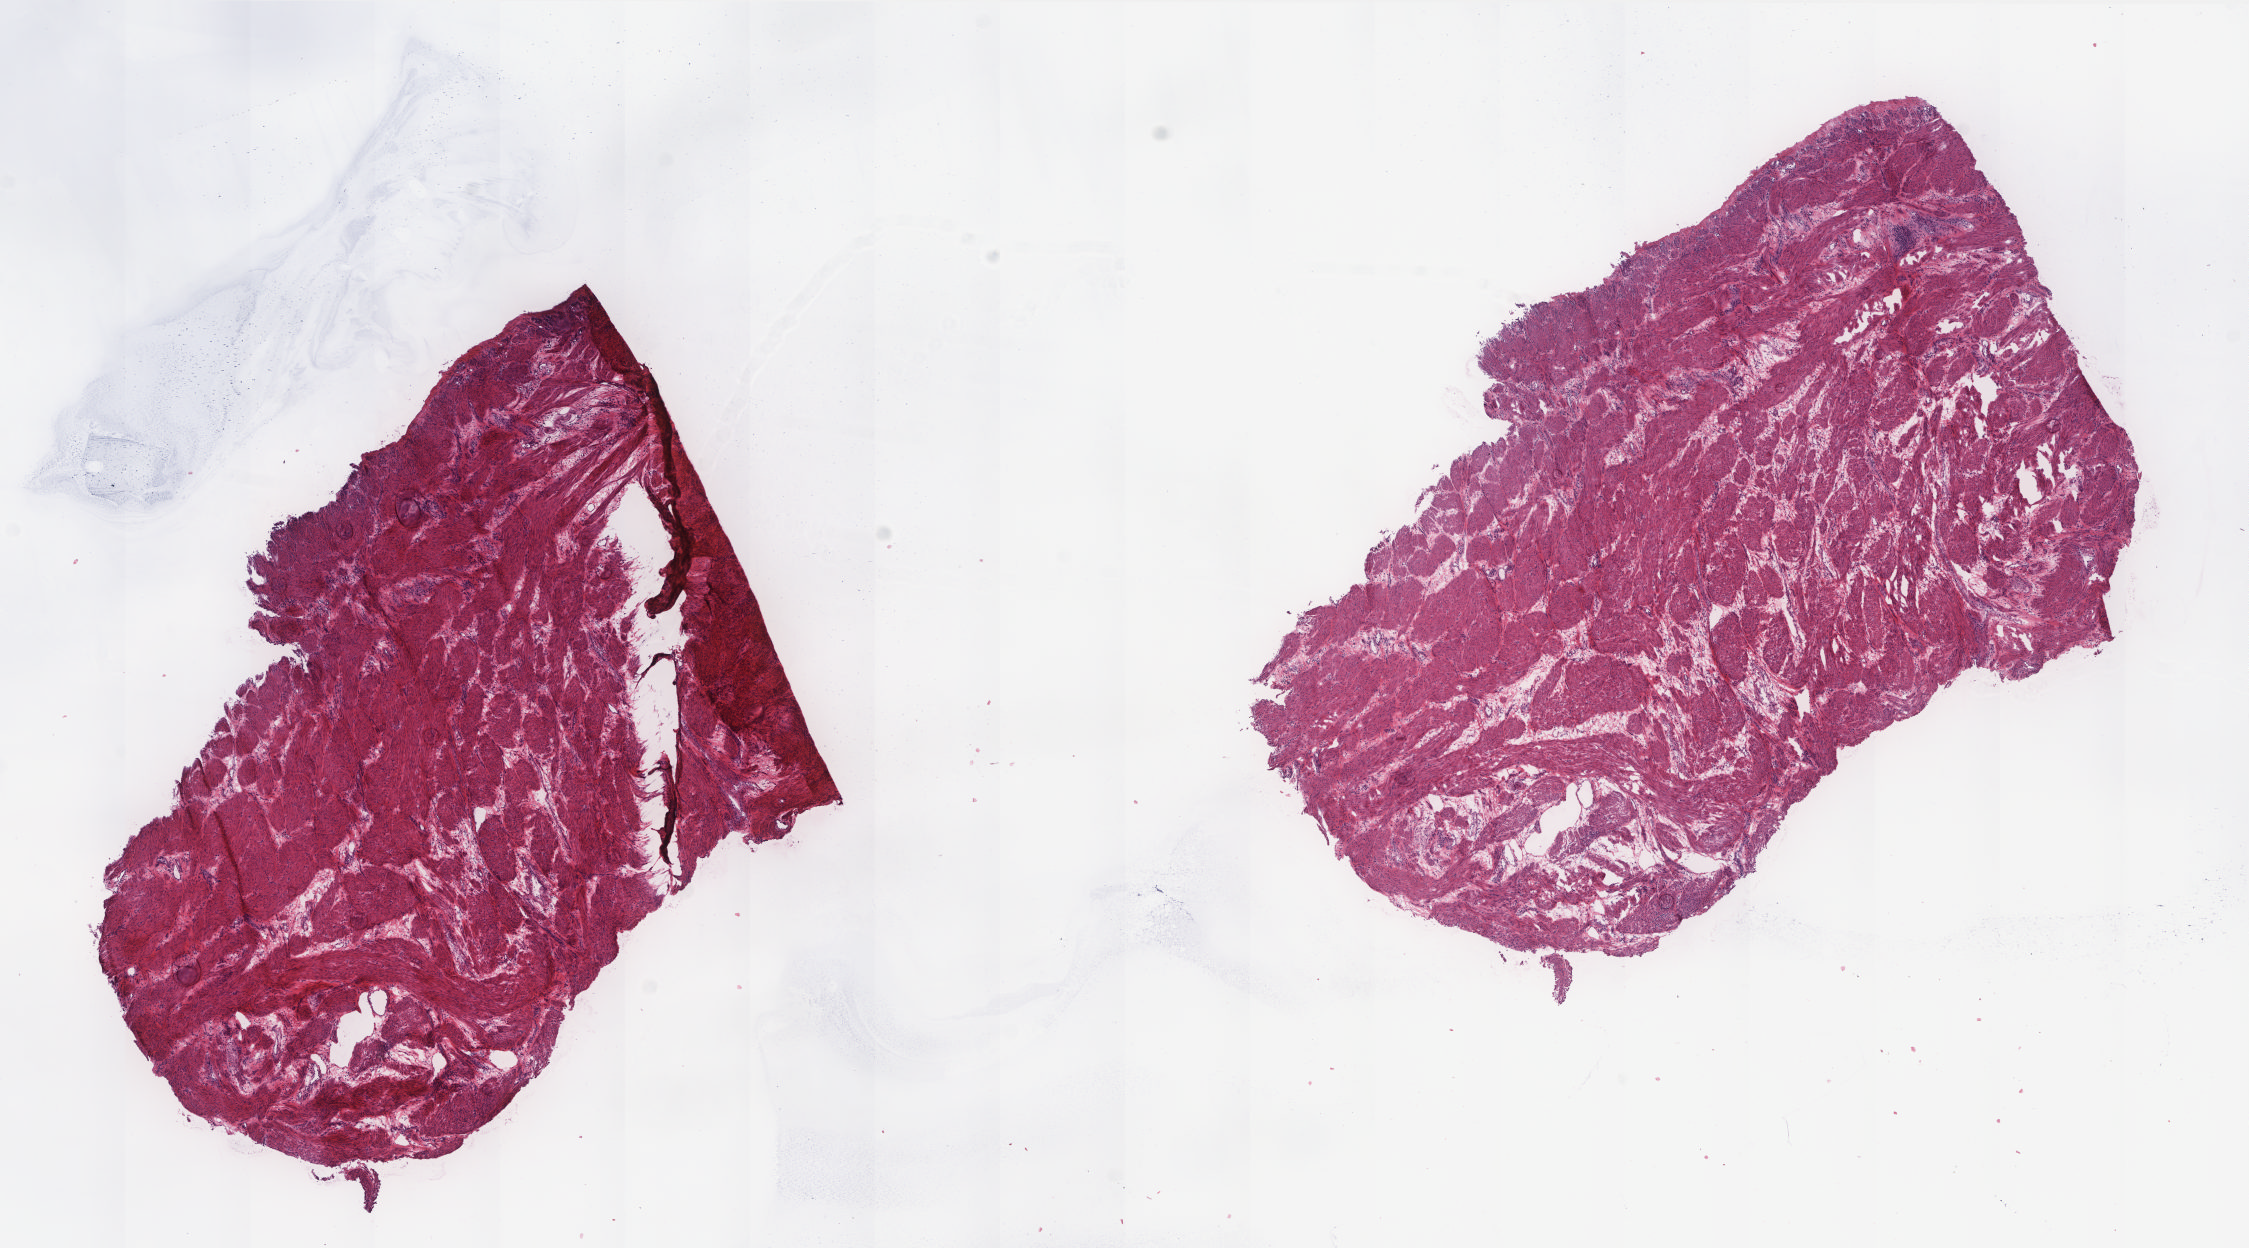
Whole-slide histology image, H&E — whole scanned area (about 18.0 x 10.0 mm, from a 20x scan) shown as a low-resolution overview. Frozen section from the top of the tissue portion. Sample: solid tissue normal (non-tumour tissue), uterus. Female, age 60 years at initial diagnosis.
This section: solid tissue normal sample (biorepository sample class). Patient diagnosis: Endometrioid adenocarcinoma, NOS (endometrium).